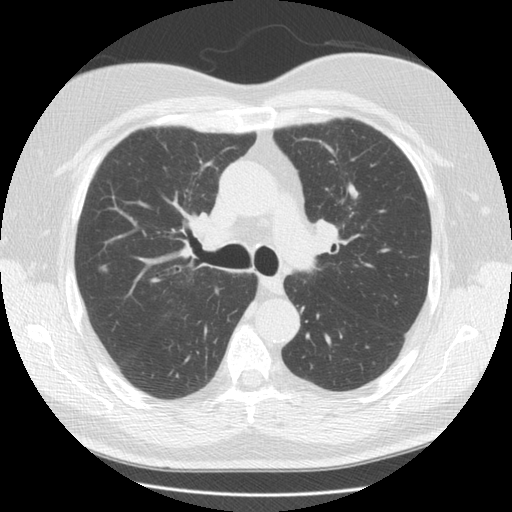
Chest CT (low-dose screening protocol), one axial image, third screening round (two years after baseline), lung window (W 1500 / L -600 HU), 2.5 mm slice thickness, slice 54 of 146 in the series. Male, age 65 years at enrolment.
Lesion marked by an expert reader, bounding box [x1, y1, x2, y2] px = [91, 256, 119, 283]. Reader record for this screening exam (exam-level; its link to the box is not recorded): non-calcified nodule or mass ≥4 mm, right upper lobe, 12 × 12 mm, smooth margins, soft tissue attenuation, pre-existing on the prior screen: yes; interval growth: yes. Official screen result: positive, other.